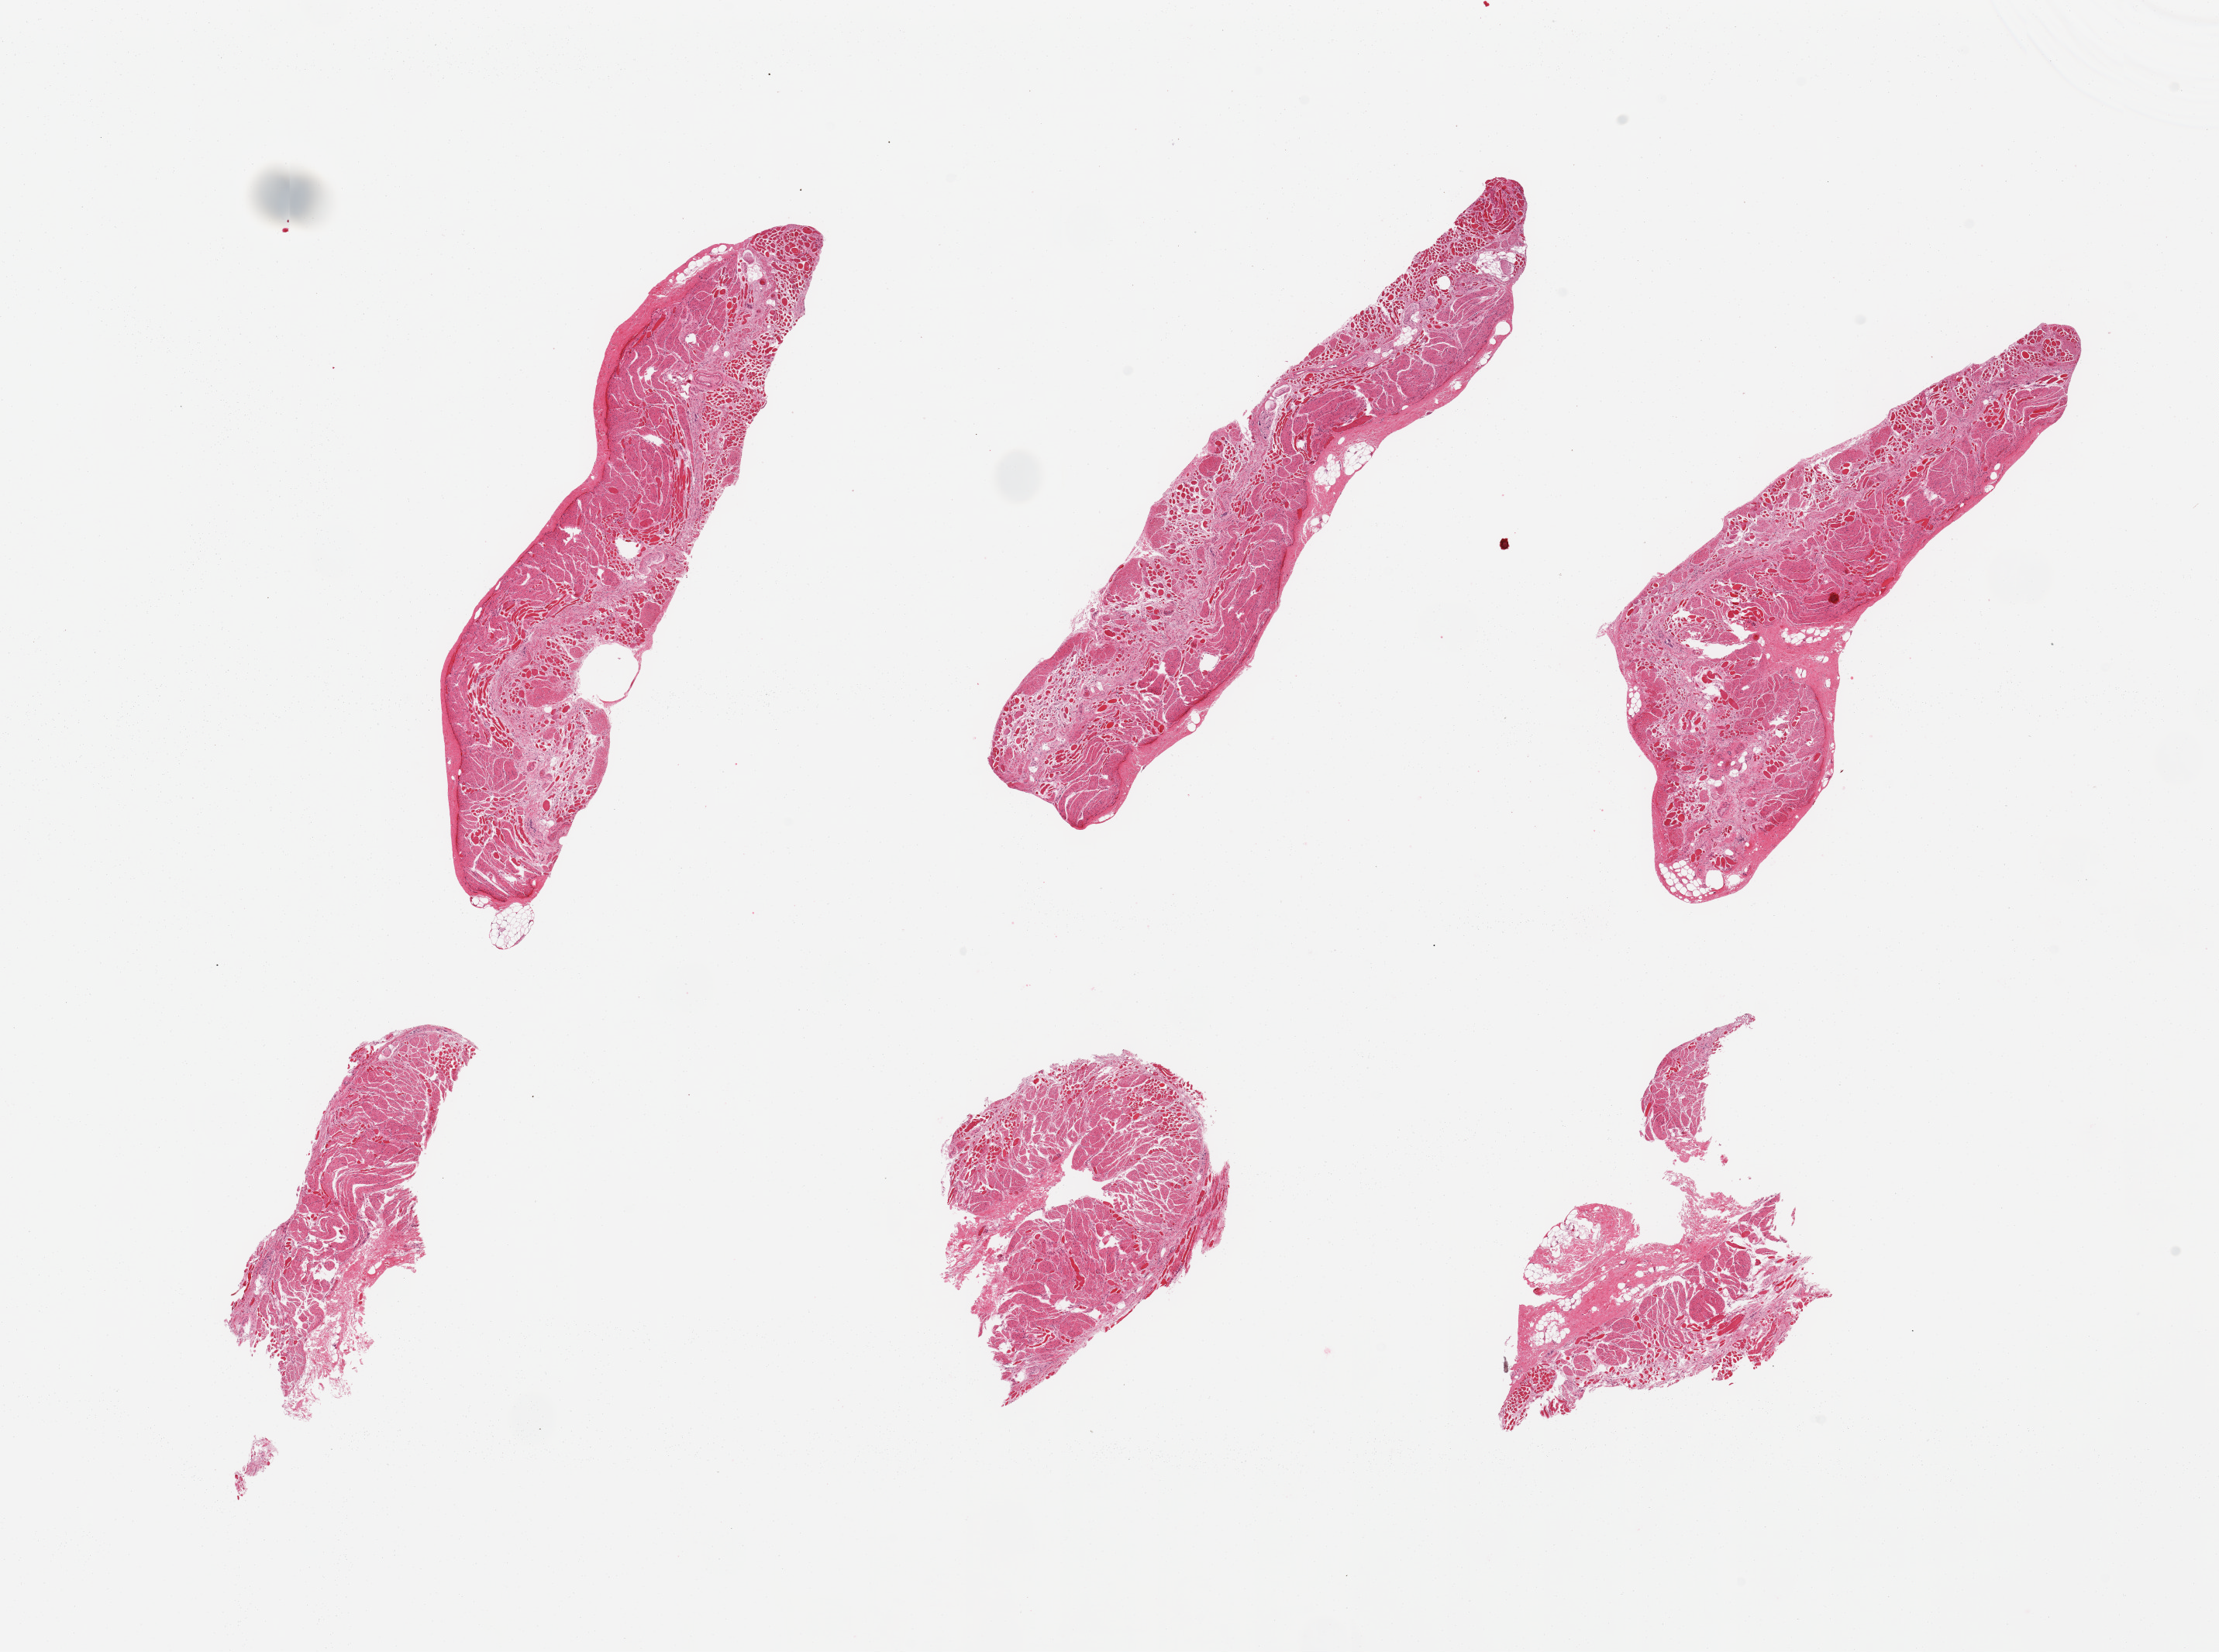
Digitized H&E-stained section — shown as a low-resolution overview of the whole scanned area (about 22.6 x 16.9 mm). PAXgene-fixed, paraffin-embedded tissue. Sampled site (target tissue): esophageal muscle. Tissue donor sample.
Reviewer comment on this tissue sample: 6 pieces, confirmed target muscularis.